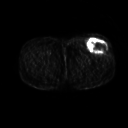
FDG PET of an extremity soft-tissue mass (from a PET/CT study), one axial slice. Slice 240 of 267 in the series (ordered by position). 128 × 128 image matrix. Male patient, age 64 years. Case-level facts recorded for this patient, not image findings: histological type: extraskeletal osteosarcoma; grade: high; site of the primary tumour: thigh.
Outlined on this slice (expert contour drawn on MRI and transferred to this co-registered scan by the dataset authors):
- gross tumour volume (mass): bounding box [x1, y1, x2, y2] px = [87, 39, 107, 53]